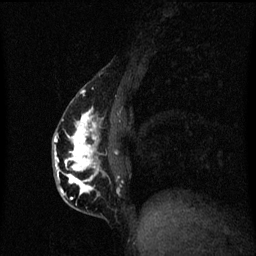
Breast MRI (dynamic contrast-enhanced), one sagittal slice; dynamic contrast-enhanced series, image 2 of 3 at this slice position (ordered by acquisition); 1.5 T; TE 4.2 ms, TR 8.4 ms; 256 × 256 image matrix, field of view 200 × 200 mm. Female patient, age 40 years.
Outlined on this slice (semi-automatically segmented with operator editing):
- analysis volume of interest (the breast-tissue region the enhancement analysis was run in; not a lesion): bounding box (x1, y1, x2, y2) in pixels: (53, 84, 116, 211)
- tumour enhancement mask (voxels above the 70 % enhancement threshold inside the analysis volume of interest): (55, 108, 103, 205)